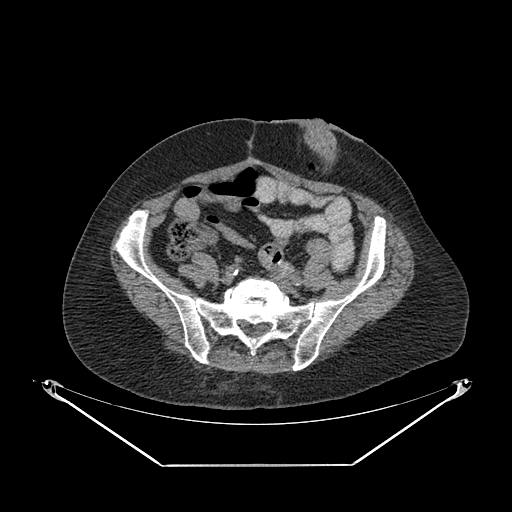
CT of an extremity soft-tissue mass (from a PET/CT study), one axial slice; position 79 of 267 along the scan axis; reconstruction kernel SOFT; 140 kVp; soft-tissue window (W 400 / L 40 HU); 3.75 mm slice thickness; 512 × 512 image matrix, field of view 500 × 500 mm. Female patient. From the clinical record (not read from this slice): histological type: spindle cell suggestive of myxofibrosarcoma; grade: intermediate; site of the primary tumour: right buttock.
Structures marked on this image (expert contour drawn on MRI and transferred to this co-registered scan by the dataset authors):
- gross tumour volume (mass): bounding box <178,352,245,392> (left, top, right, bottom; pixels)